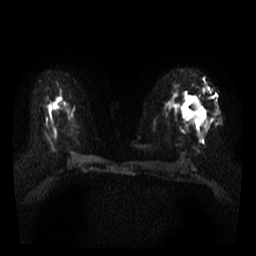
Breast MRI, one axial slice. Position 20 of 36 along the scan axis. Diffusion-weighted series; image 2 of 4 stored at this slice position (different b-values; order by instance number). 3 T. 5 mm slice thickness. 256 × 256 image matrix, field of view 300 × 300 mm. Female patient.
Structures marked on this image (manually delineated by an expert):
- tumour on diffusion-weighted imaging: box from (x=181, y=99) to (x=204, y=124) px